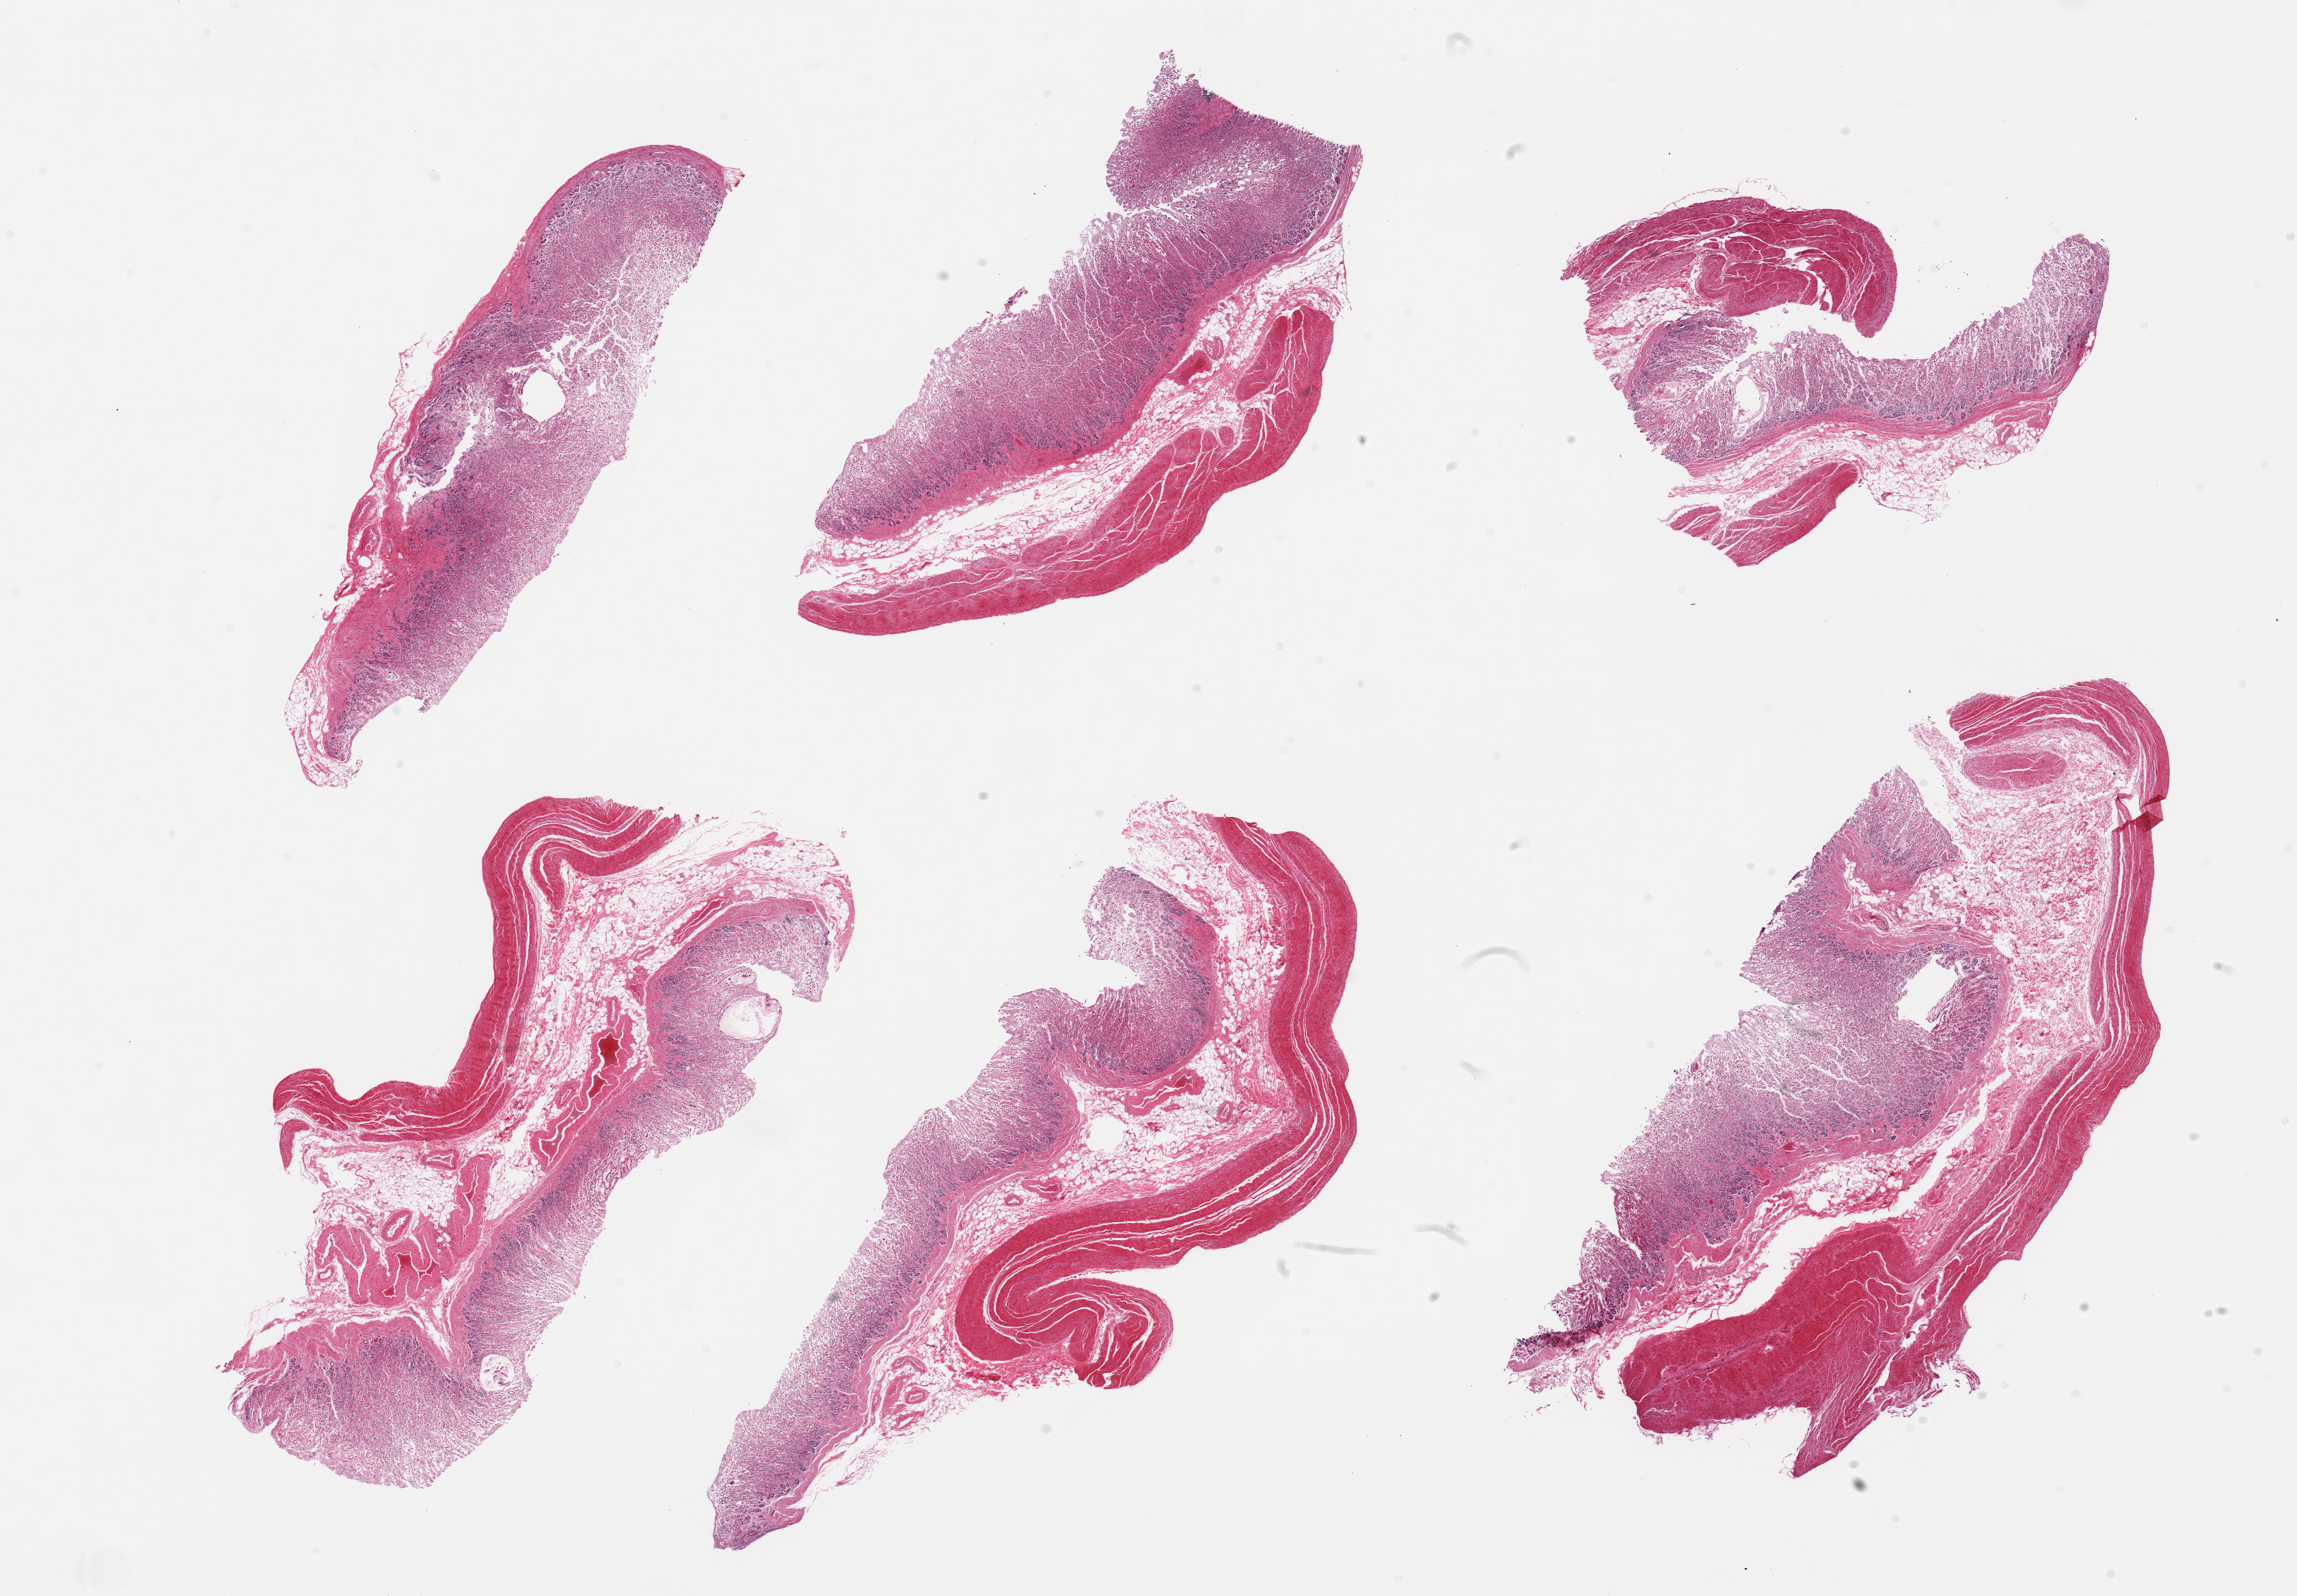
Whole-slide image, hematoxylin and eosin (H&E) stain, brightfield — low-resolution overview of the scanned area, about 26.6 x 18.5 mm. PAXgene-fixed paraffin-embedded (PFPE) section. Sampled site (target tissue): stomach. Donor tissue sample.
Reviewer comment on this tissue sample: 6 pieces; mucosa largely autolyzed; muscle intact without fibrosis.